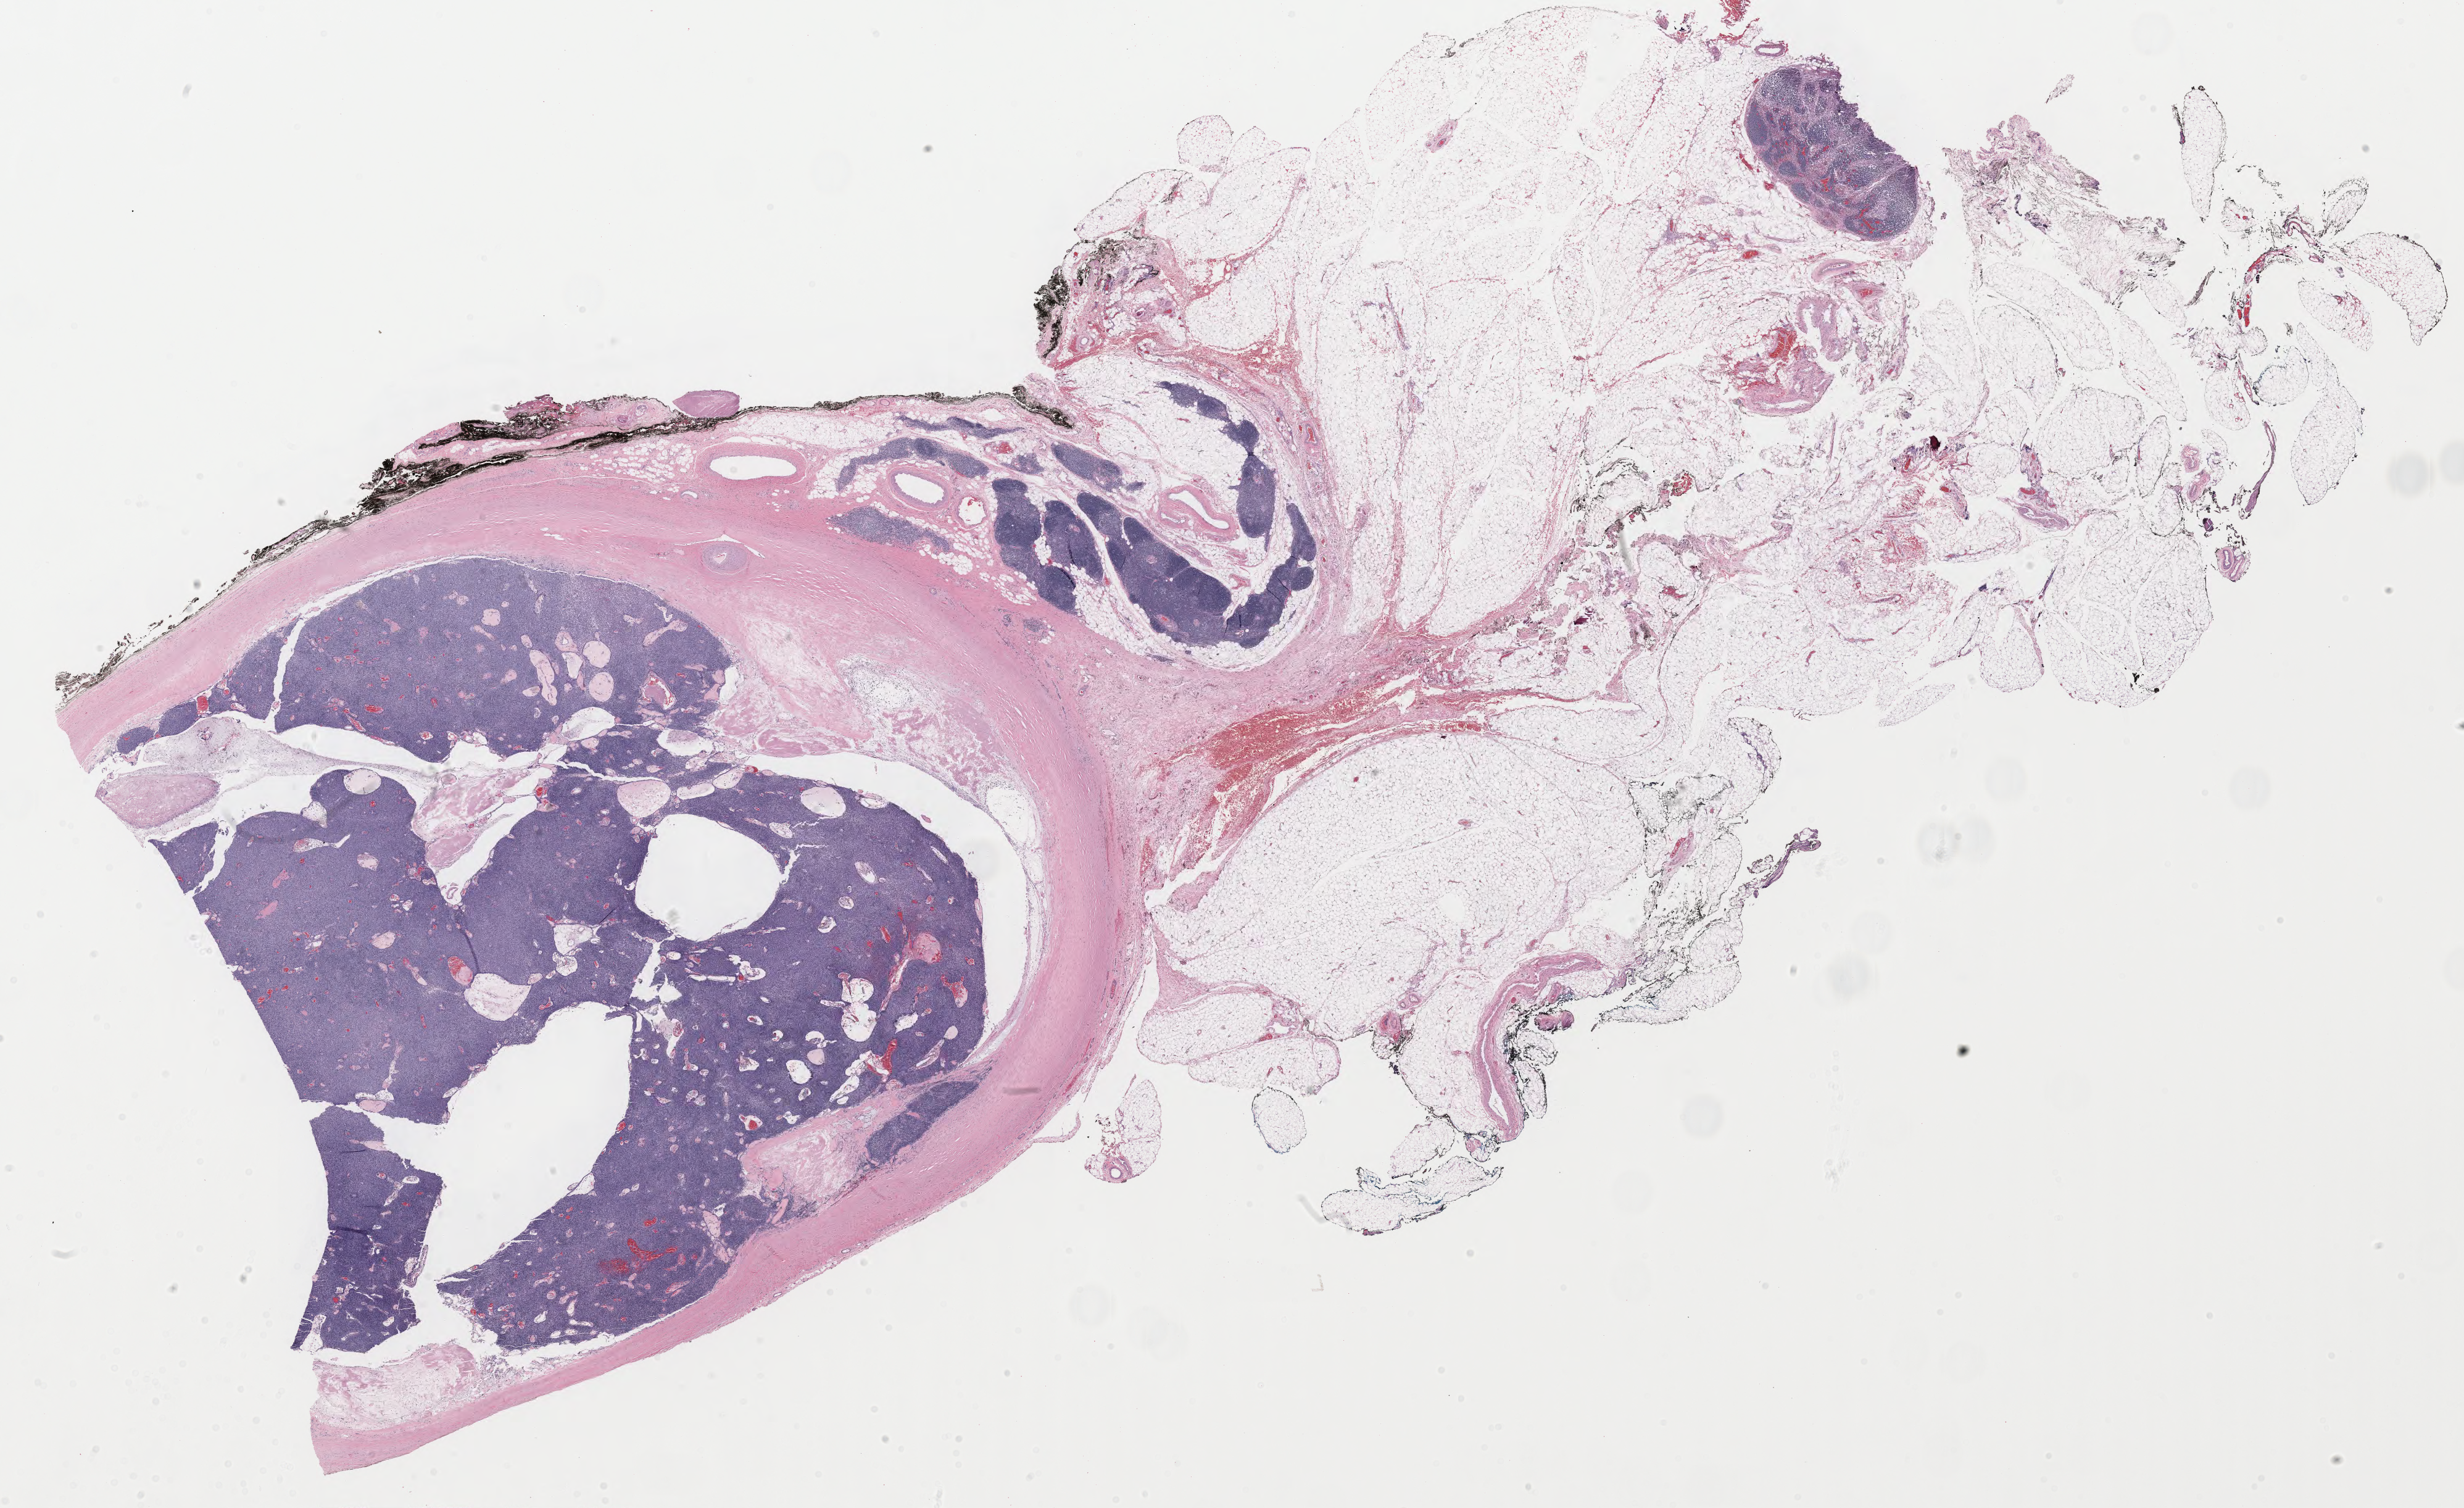
Hematoxylin and eosin (H&E) stained whole-slide image — low-resolution overview of the scanned area, about 31.7 x 19.4 mm. FFPE section. Primary tumour sample from the thymus. Female, age 43 years at initial diagnosis.
- pathologic diagnosis: Thymoma, type B2, malignant